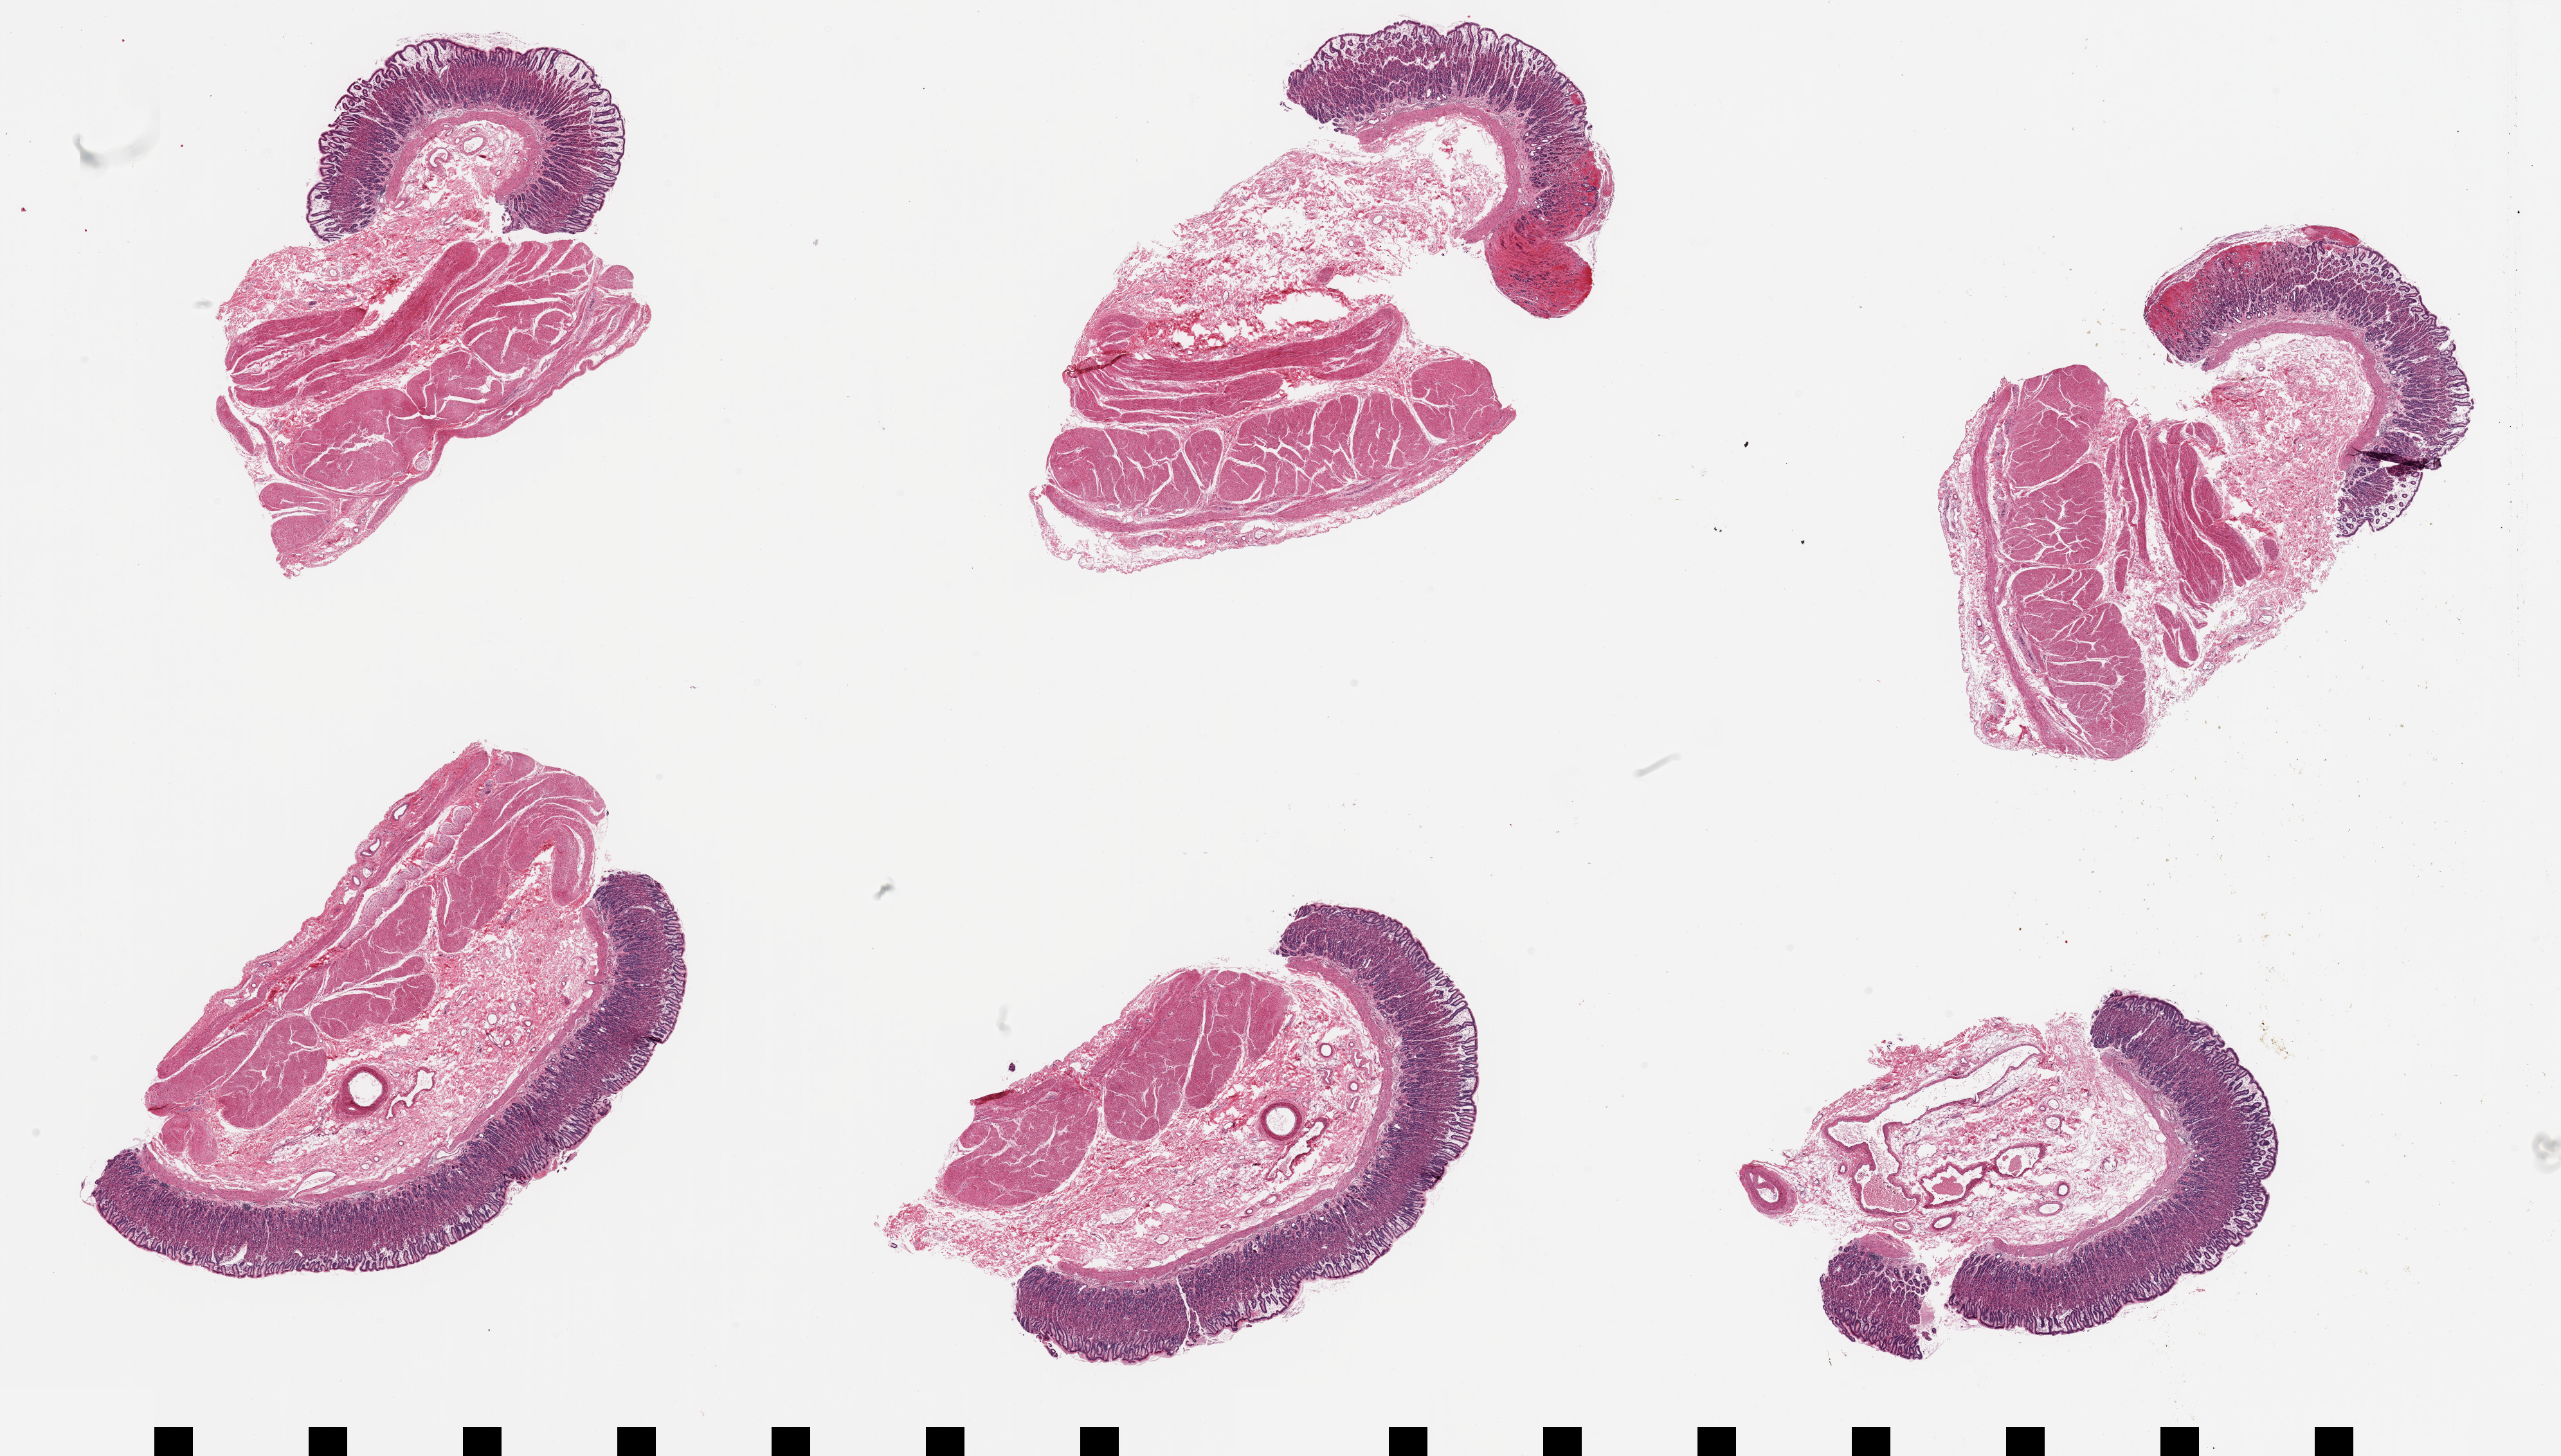
Haematoxylin and eosin whole-slide image, a low-resolution overview of the entire scanned area, about 31.5 x 17.9 mm (slide scanned at 20x). PAXgene-fixed paraffin-embedded (PFPE) section. Section of stomach (target tissue). Tissue donor sample.
- pathologist's review note for this sample: 6 pieces, mucosa generally well- preserved, foci ischemic damage/gastritis; Mucosa is ~25% thickness